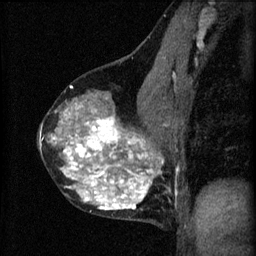
Breast MRI (dynamic contrast-enhanced), one sagittal slice. Slice 35 of 60 in the series (ordered by position). 3 images stored at this slice position (order not interpretable as contrast timing). 1.5 T. TE 4.2 ms, TR 8.2 ms. 2 mm slice thickness. 256 × 256 image matrix. Patient: female, 40 years.
Annotated regions visible in this slice (semi-automatic segmentation, software-assisted and operator-edited):
- analysis volume of interest (the breast-tissue region the enhancement analysis was run in; not a lesion): bounding box <38,76,179,219> (left, top, right, bottom; pixels)
- tumour enhancement mask (voxels above the 70 % enhancement threshold inside the analysis volume of interest): <52,108,165,211>